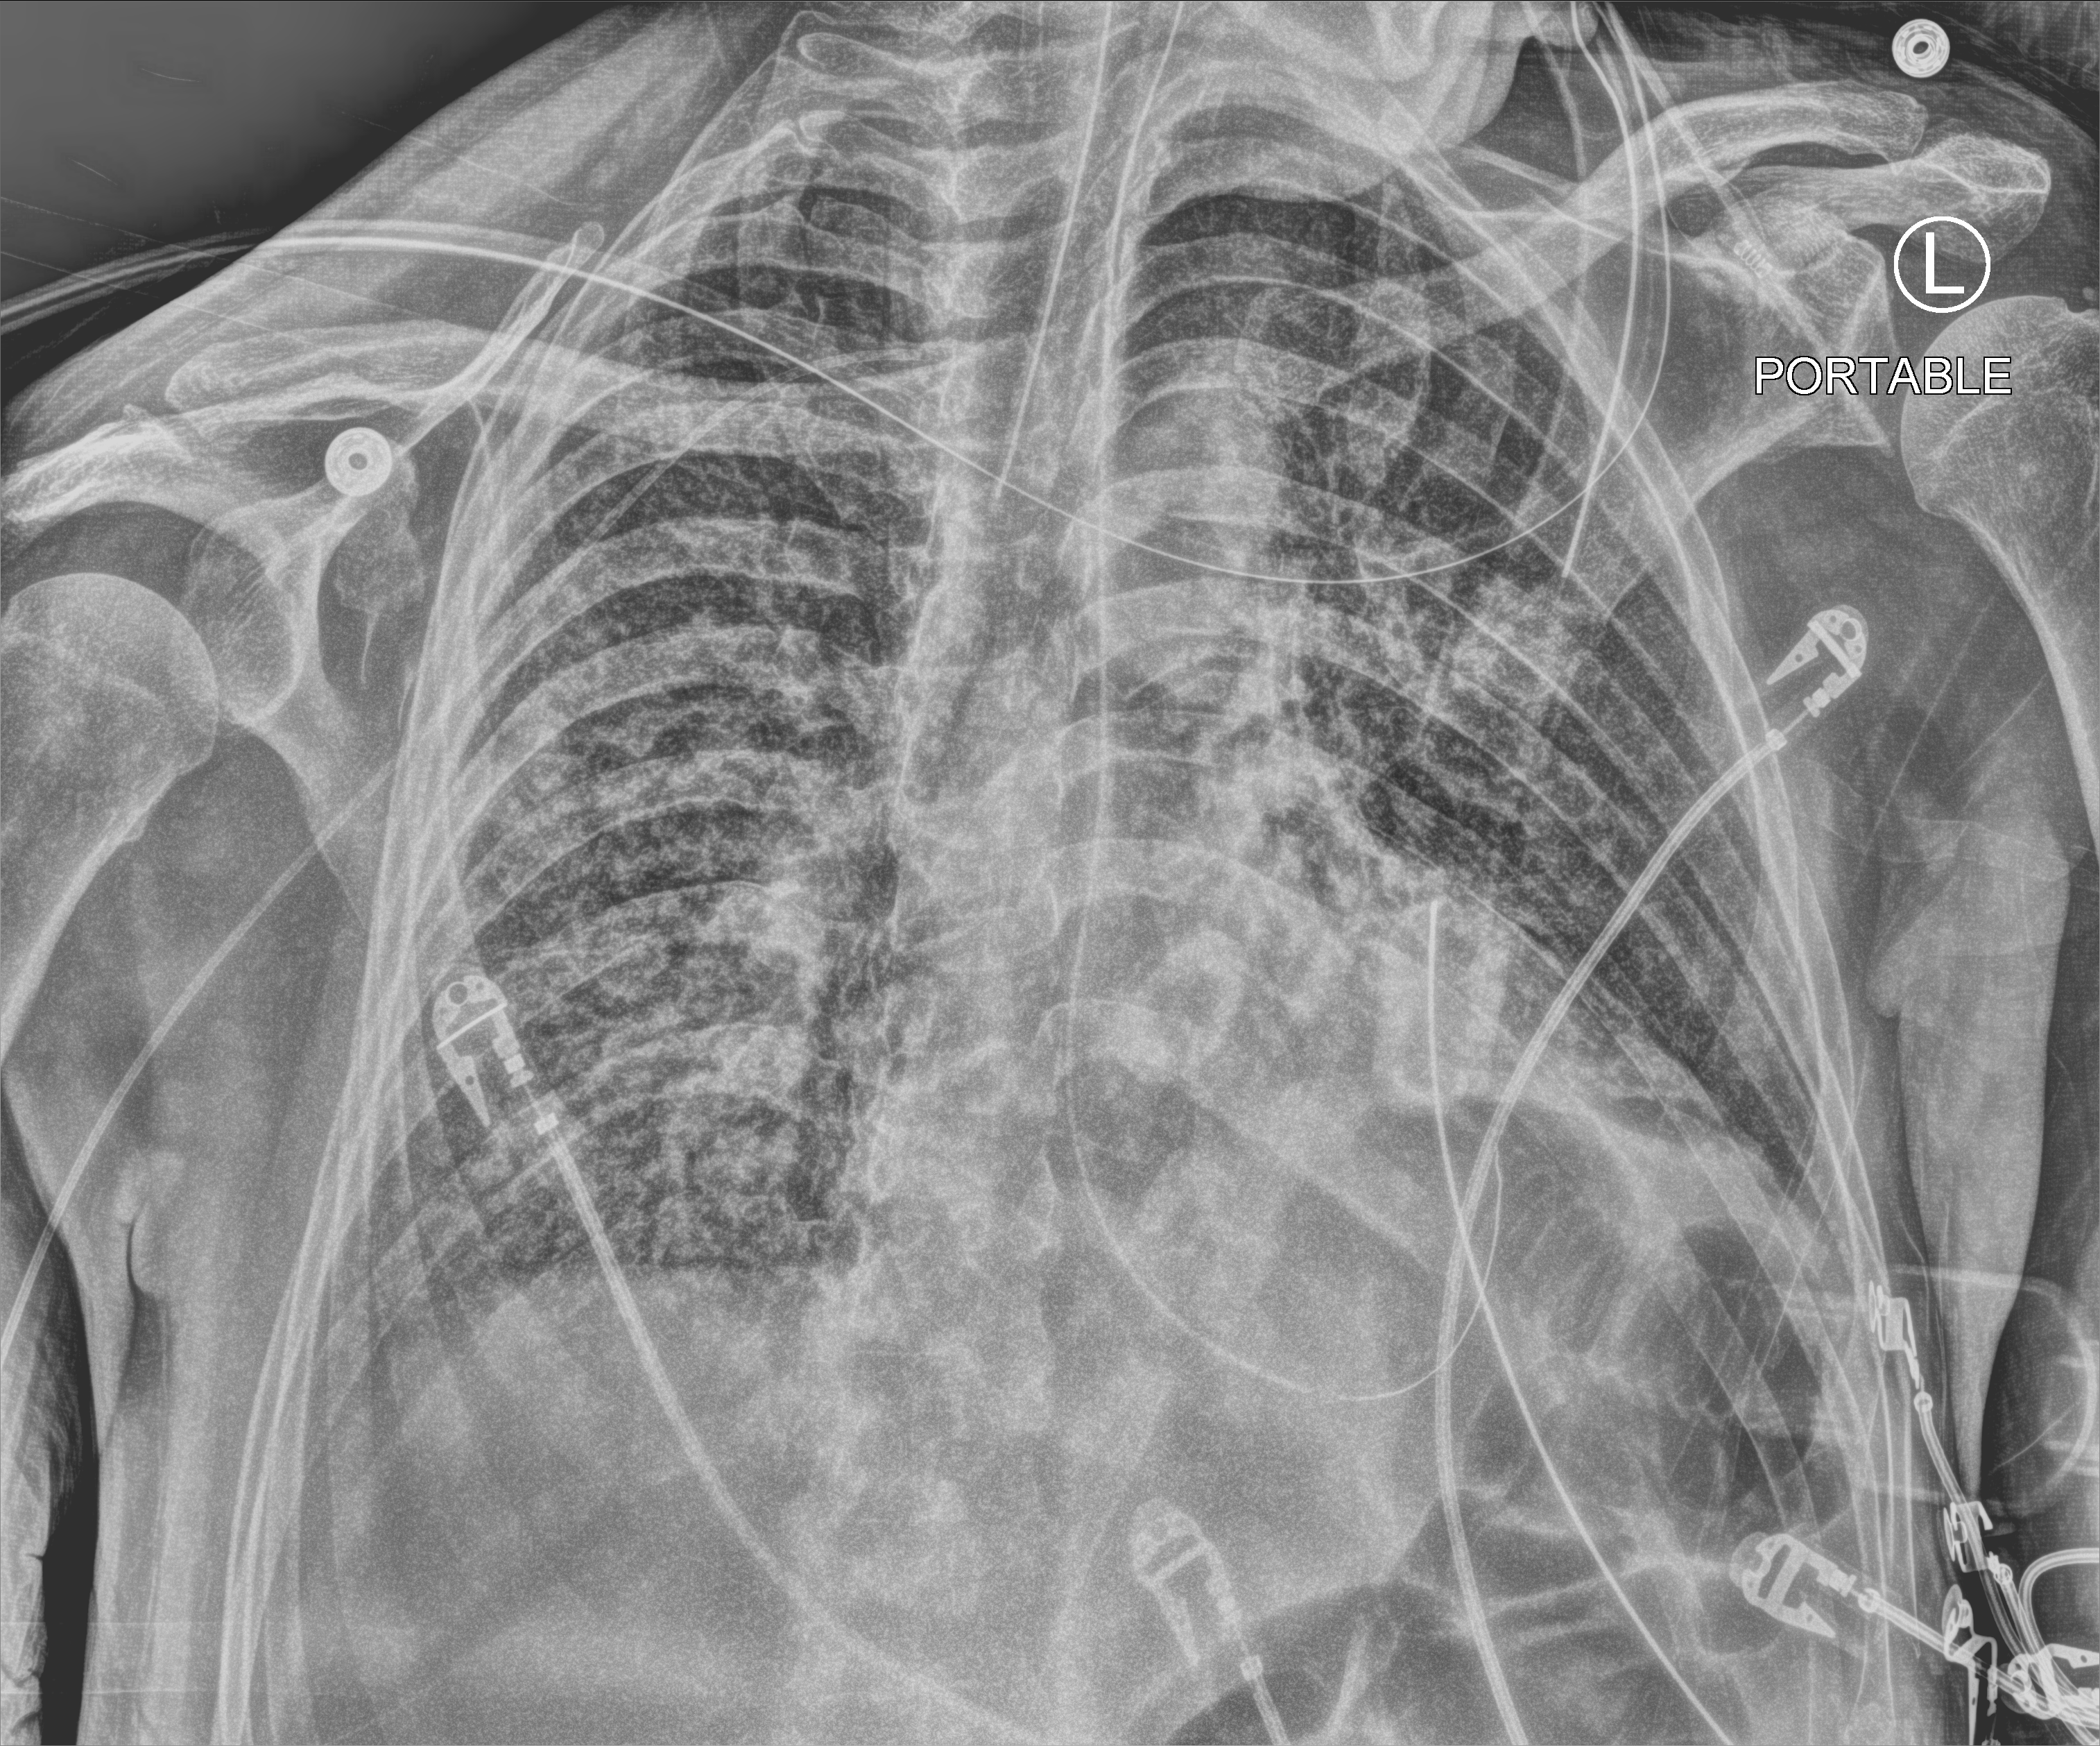
Portable chest radiograph; anteroposterior (AP) projection. Patient hospitalised with COVID-19; male, aged 60–74 years.
From the hospital-stay record, not from the radiograph (when in the stay this image was taken is not recorded):
- other chronic lung disease (admission record): no